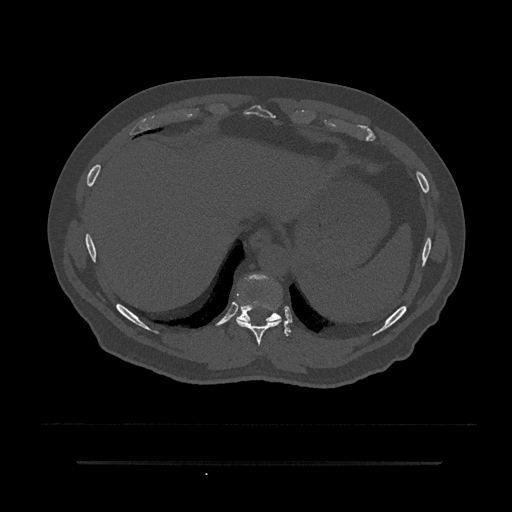
CT including the spine, one axial slice; reconstruction kernel Br40s/3; 120 kVp; bone window (W 1800 / L 400 HU); 0.5 mm slice thickness; 512 × 512 image matrix. Patient: male, 59 years. Case-level facts recorded for this patient, not image findings: primary cancer: bile ducts.
Annotated regions visible in this slice (semi-automatic segmentation, software-assisted and operator-edited):
- T10 vertebra: bounding box [x1, y1, x2, y2] px = [236, 274, 291, 336]
- T9 vertebra: [236, 307, 281, 345]